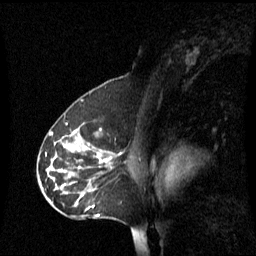
Breast MRI (dynamic contrast-enhanced), one sagittal slice; position 38 of 60 along the scan axis; dynamic contrast-enhanced series, image 2 of 3 at this slice position (ordered by acquisition); 1.5 T; TE 4.2 ms, TR 8.4 ms; 2.2 mm slice thickness; 256 × 256 image matrix. Patient: female, 45 years. Case-level facts recorded for this patient, not image findings: setting: breast cancer imaged before/during neoadjuvant chemotherapy; receptor status: HR-positive, HER2-negative.
Structures marked on this image (semi-automatically segmented with operator editing):
- analysis volume of interest (the breast-tissue region the enhancement analysis was run in; not a lesion): bounding box (x1, y1, x2, y2) in pixels: (38, 122, 123, 219)
- tumour enhancement mask (voxels above the 70 % enhancement threshold inside the analysis volume of interest): (72, 130, 107, 217)